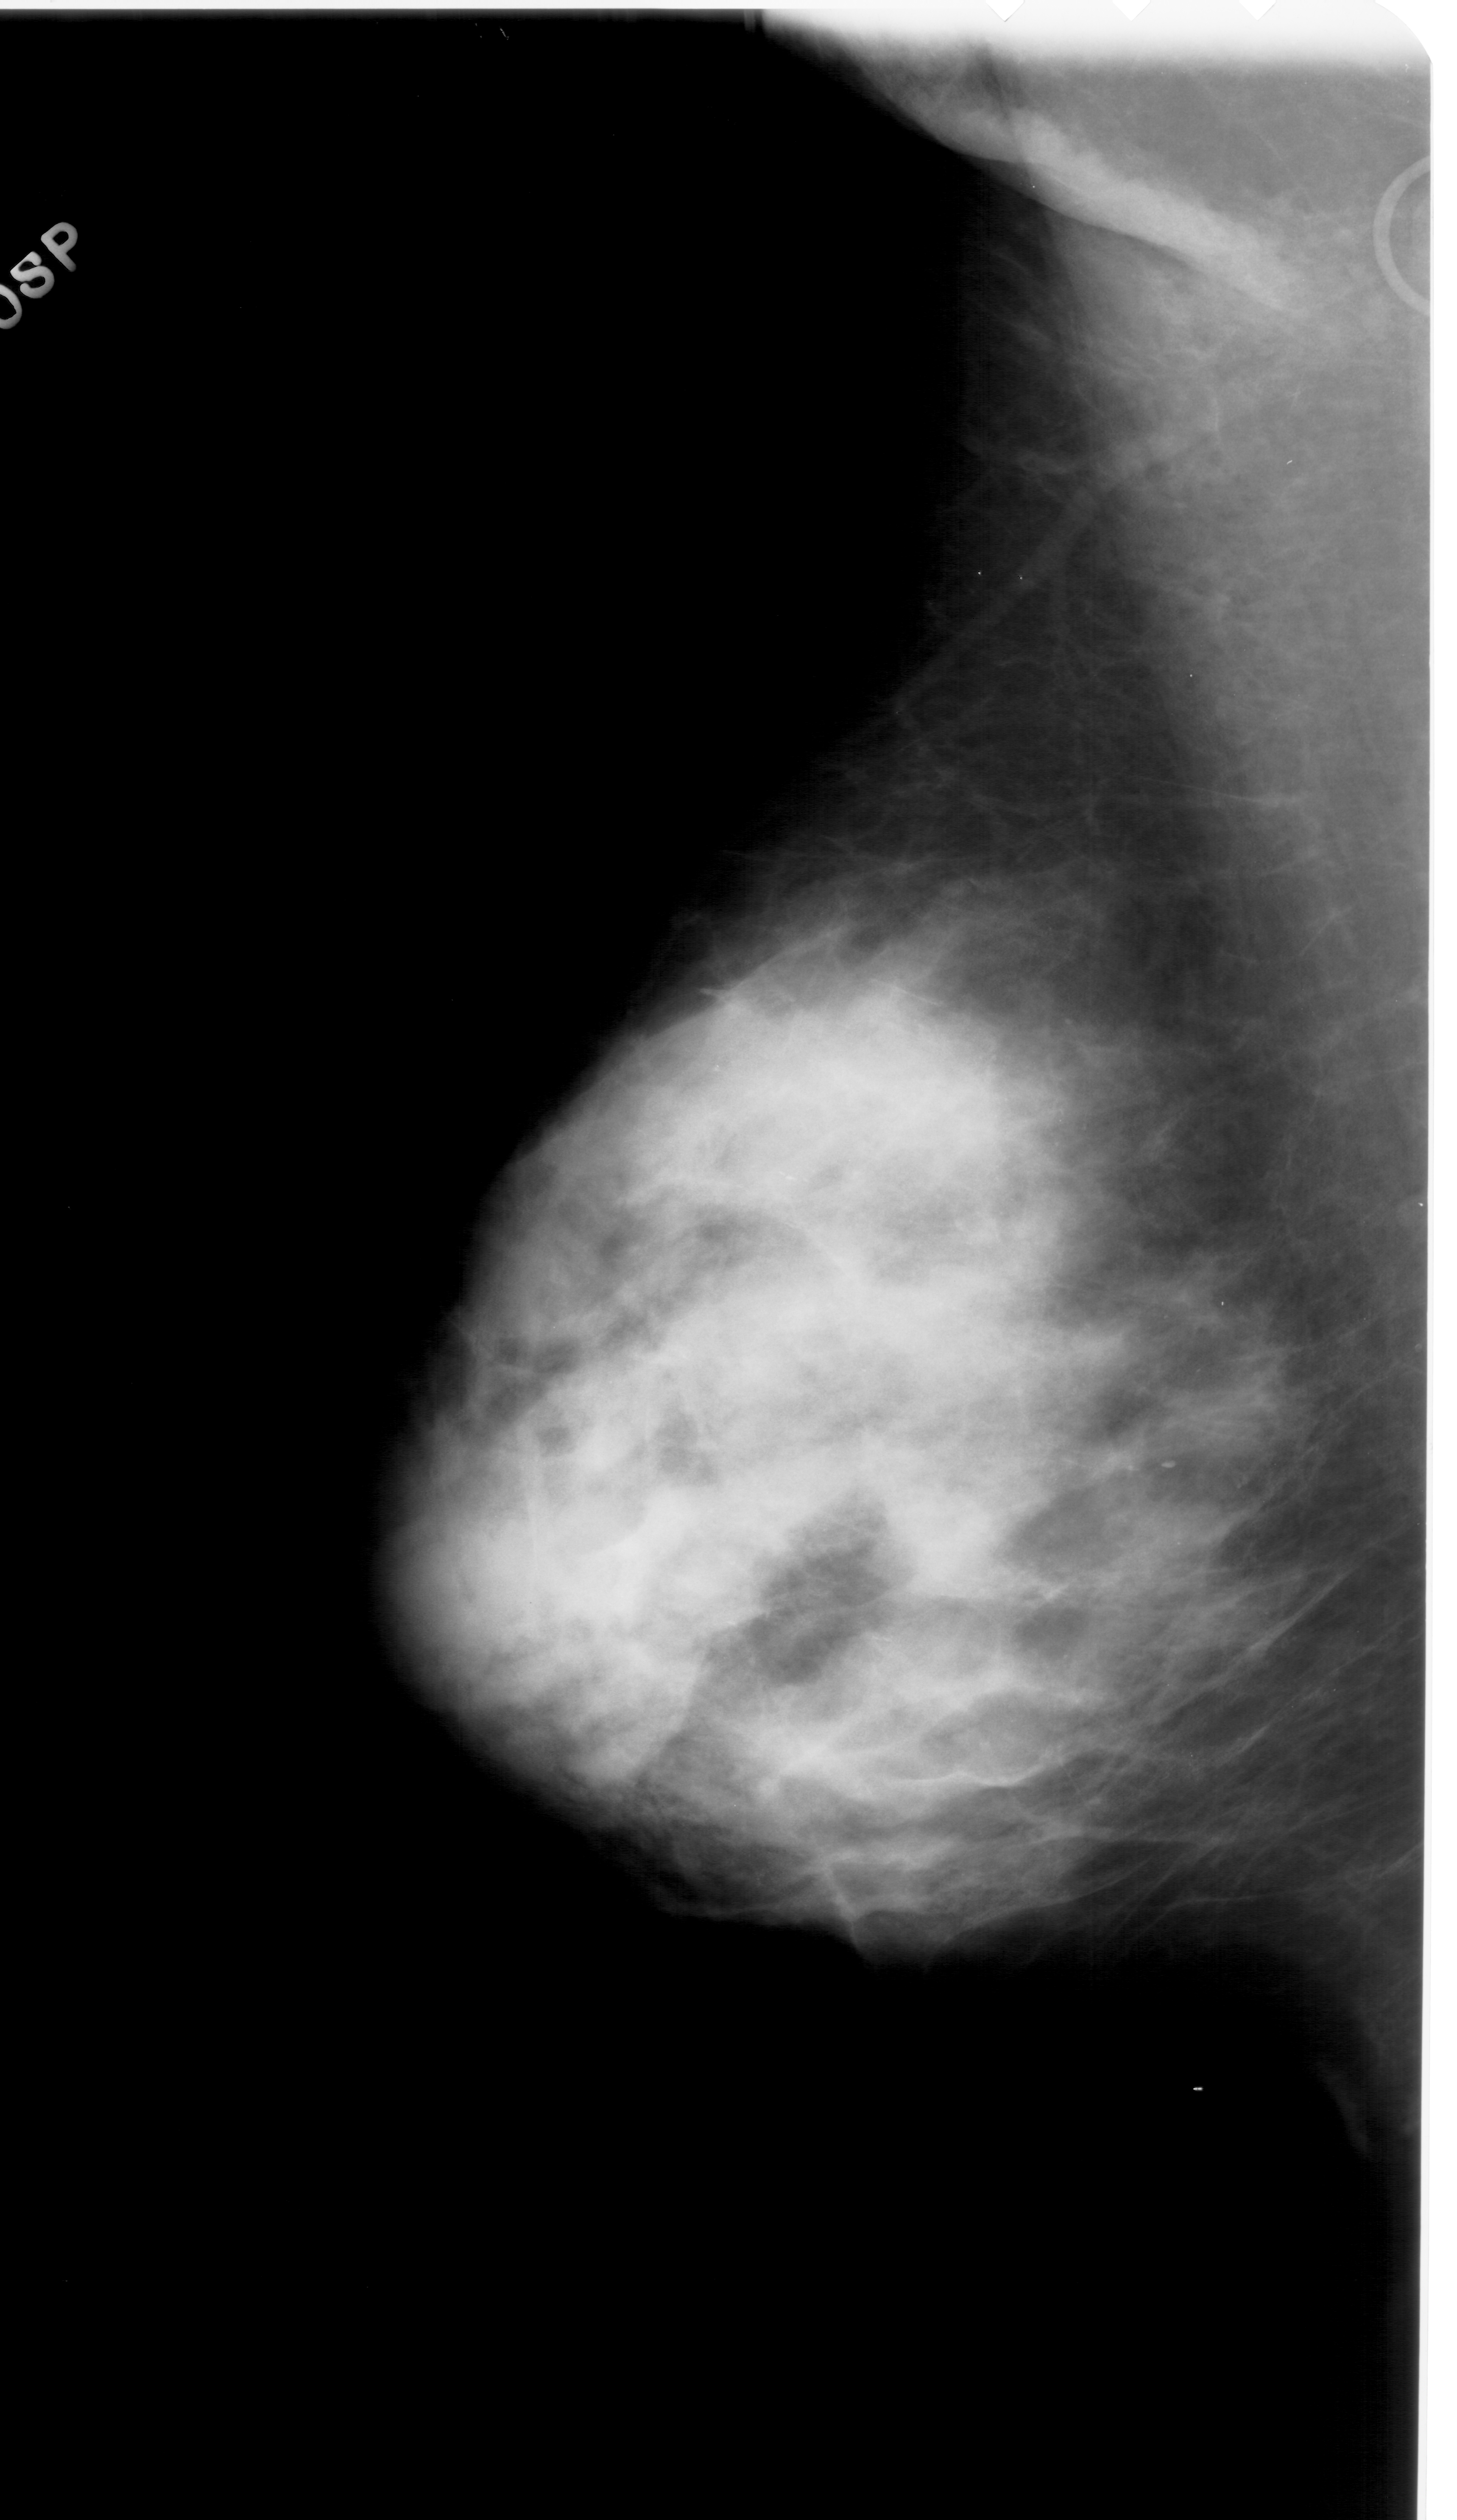
Mammogram (digitized film); left breast; MLO view; BI-RADS breast density category 4 (scale 1–4); 1457 × 2520 image matrix.
Marked abnormalities (boxes around the expert regions of interest):
- calcifications, morphology pleomorphic, distribution clustered; BI-RADS assessment category 4; pathology result (as recorded, not read from the image): benign: bounding box [x1, y1, x2, y2] px = [768, 1155, 838, 1194]